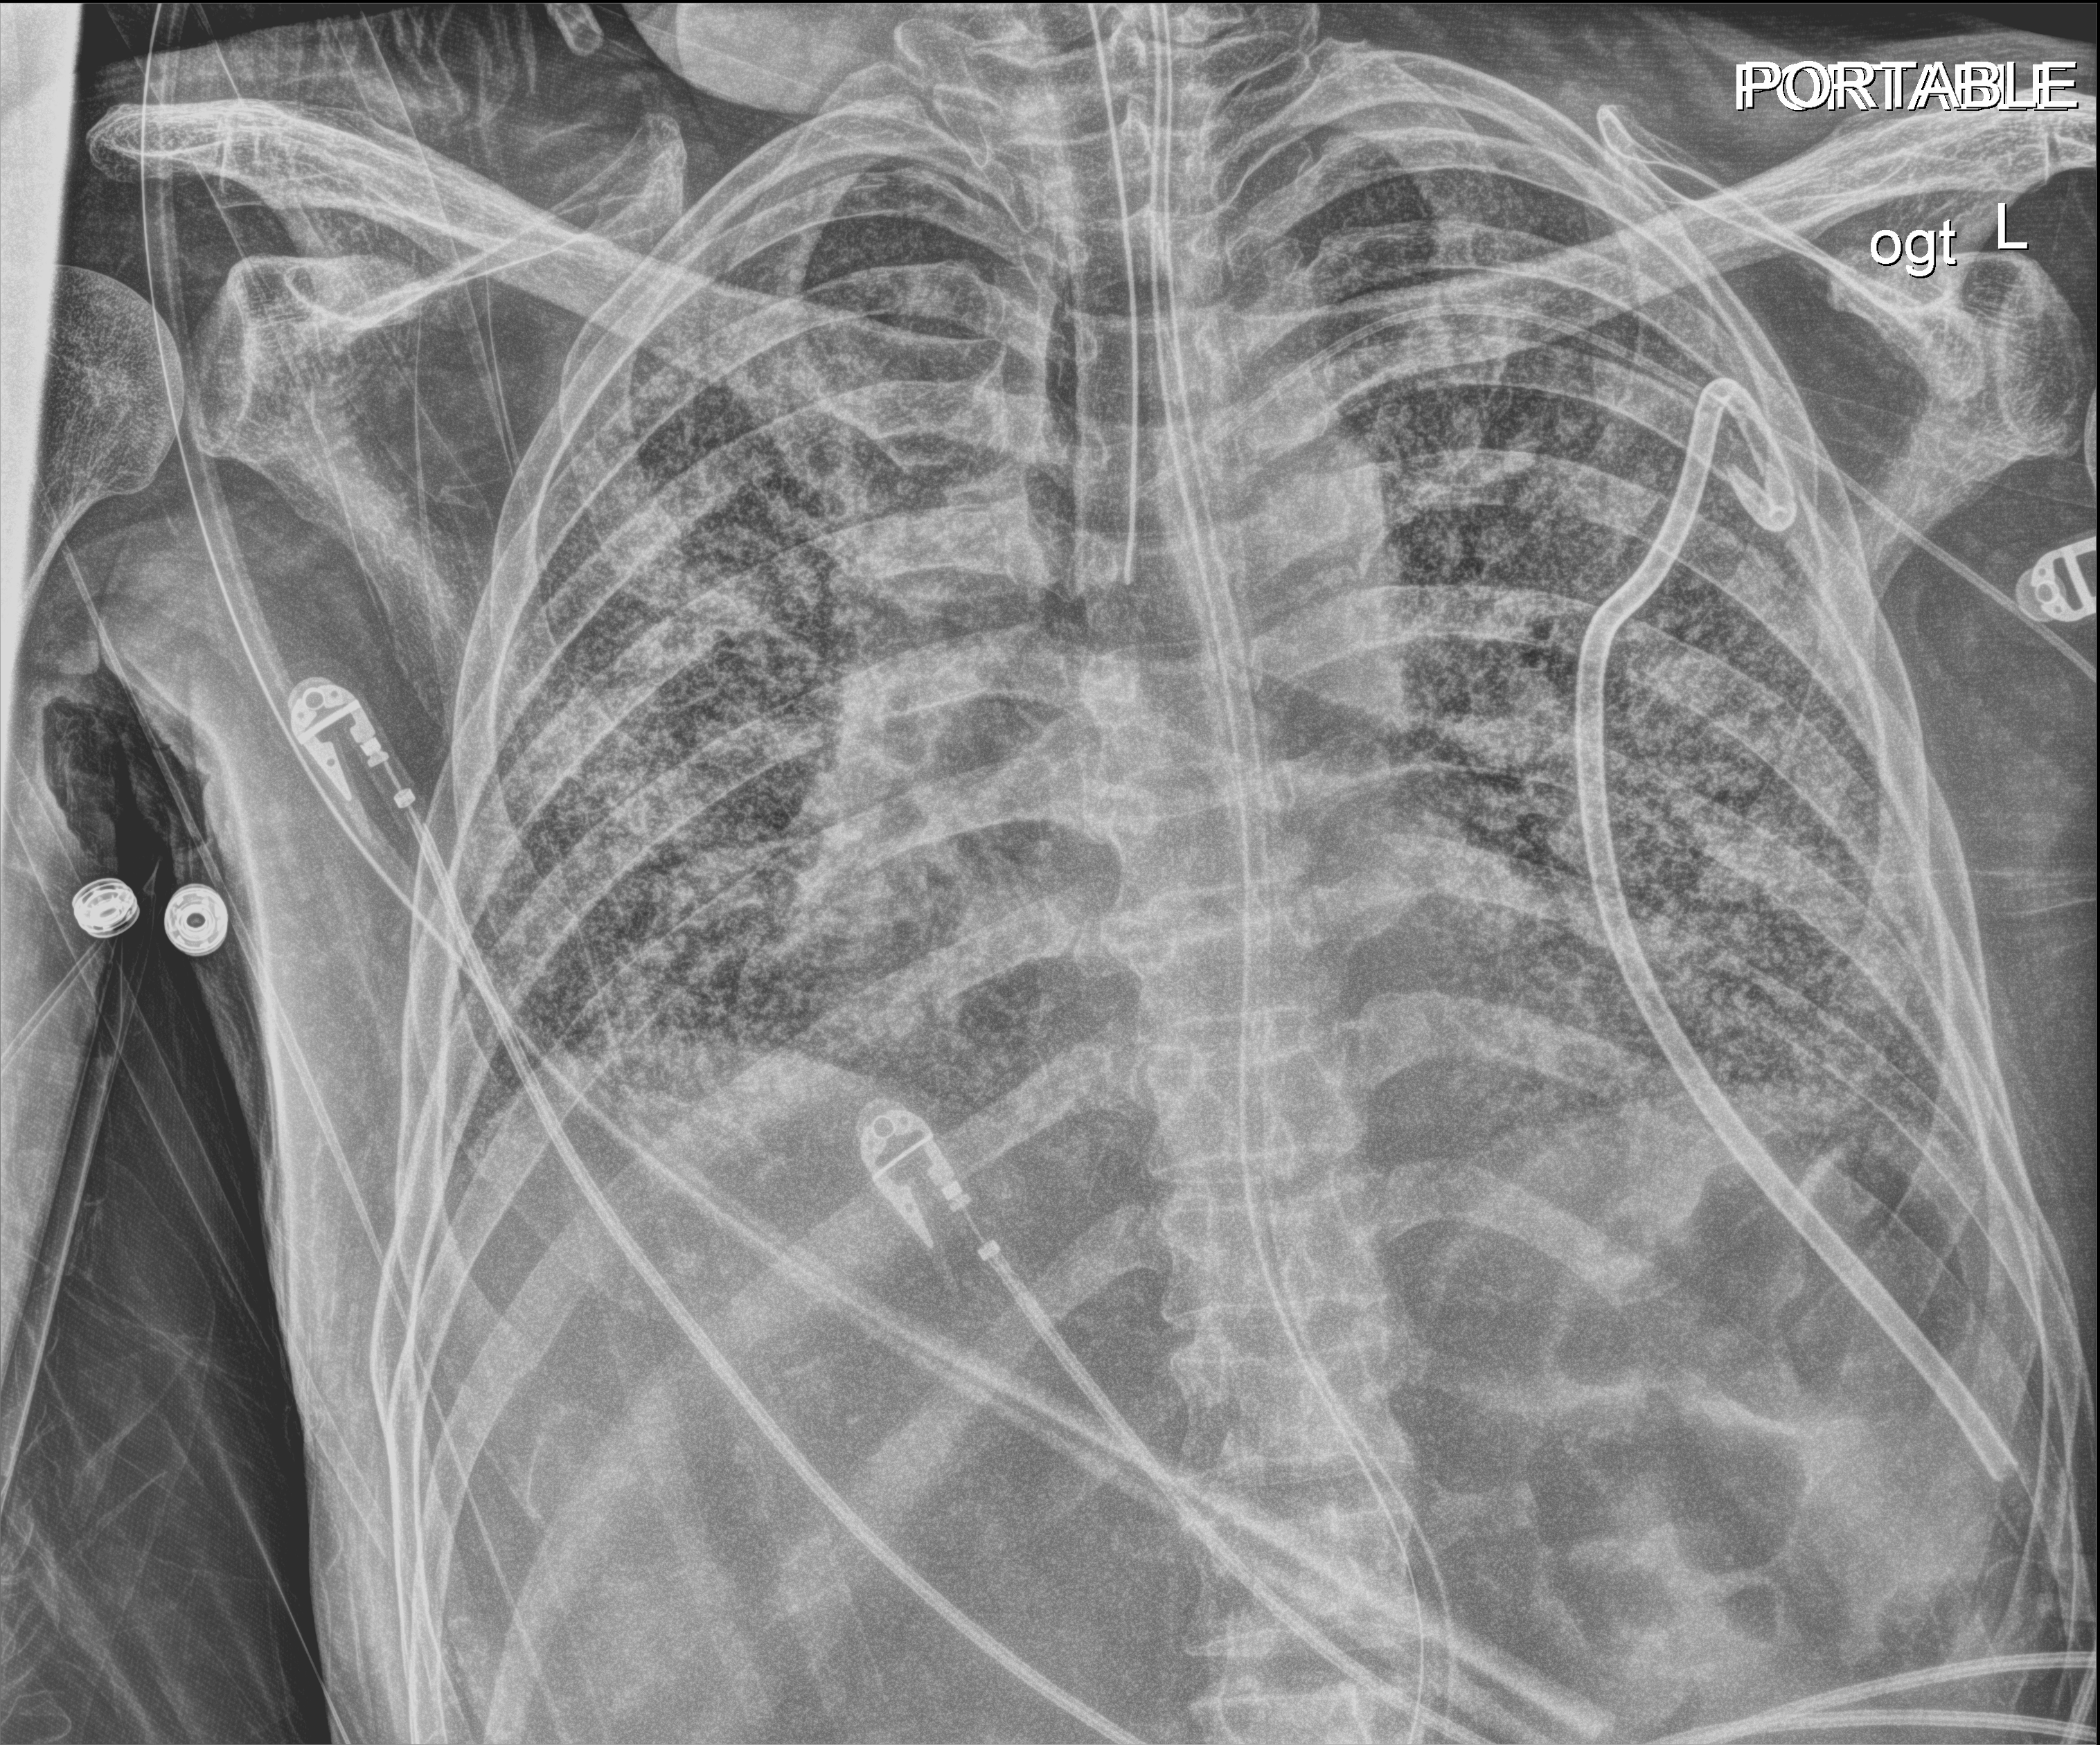
Chest X-ray, anteroposterior (AP) projection. Male patient hospitalised with COVID-19, age 60–74 years.
Hospital-stay facts (about this admission, not read from this image; timing relative to this image not recorded): mechanically ventilated during this hospital stay: yes.